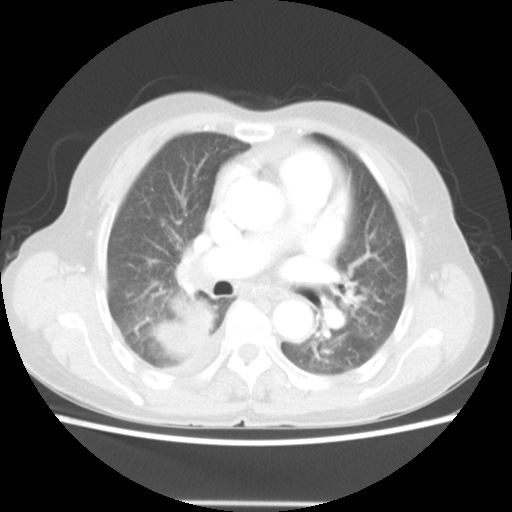
Chest CT, one axial slice. Position 29 of 52 along the scan axis. Reconstruction kernel STANDARD. 140 kVp. Lung window (W 1500 / L -600 HU). 5 mm slice thickness. 512 × 512 image matrix, field of view 337 × 337 mm. Female patient, age 67 years. Case-level facts recorded for this patient, not image findings: clinical TNM (as recorded): T3 N1 M1.
Structures marked on this image (rectangle marked by the reading radiologist):
- lung tumour (recorded histology: adenocarcinoma): bounding box [x1, y1, x2, y2] px = [152, 295, 211, 362]